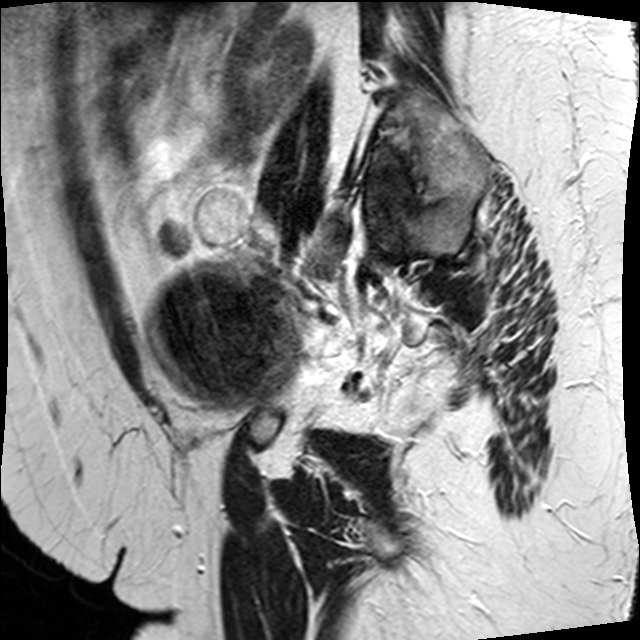
Pelvic MRI for cervical cancer, one sagittal slice. Slice 8 of 34 in the series (ordered by position). T2-weighted. 1.5 T. TE 89 ms, TR 3320 ms. 4 mm slice thickness. 640 × 640 image matrix, field of view 260 × 260 mm. Patient: female, 50 years.
Outlined on this slice (expert manual segmentation):
- uterus and cervix: bounding box [x1, y1, x2, y2] px = [148, 257, 300, 406]